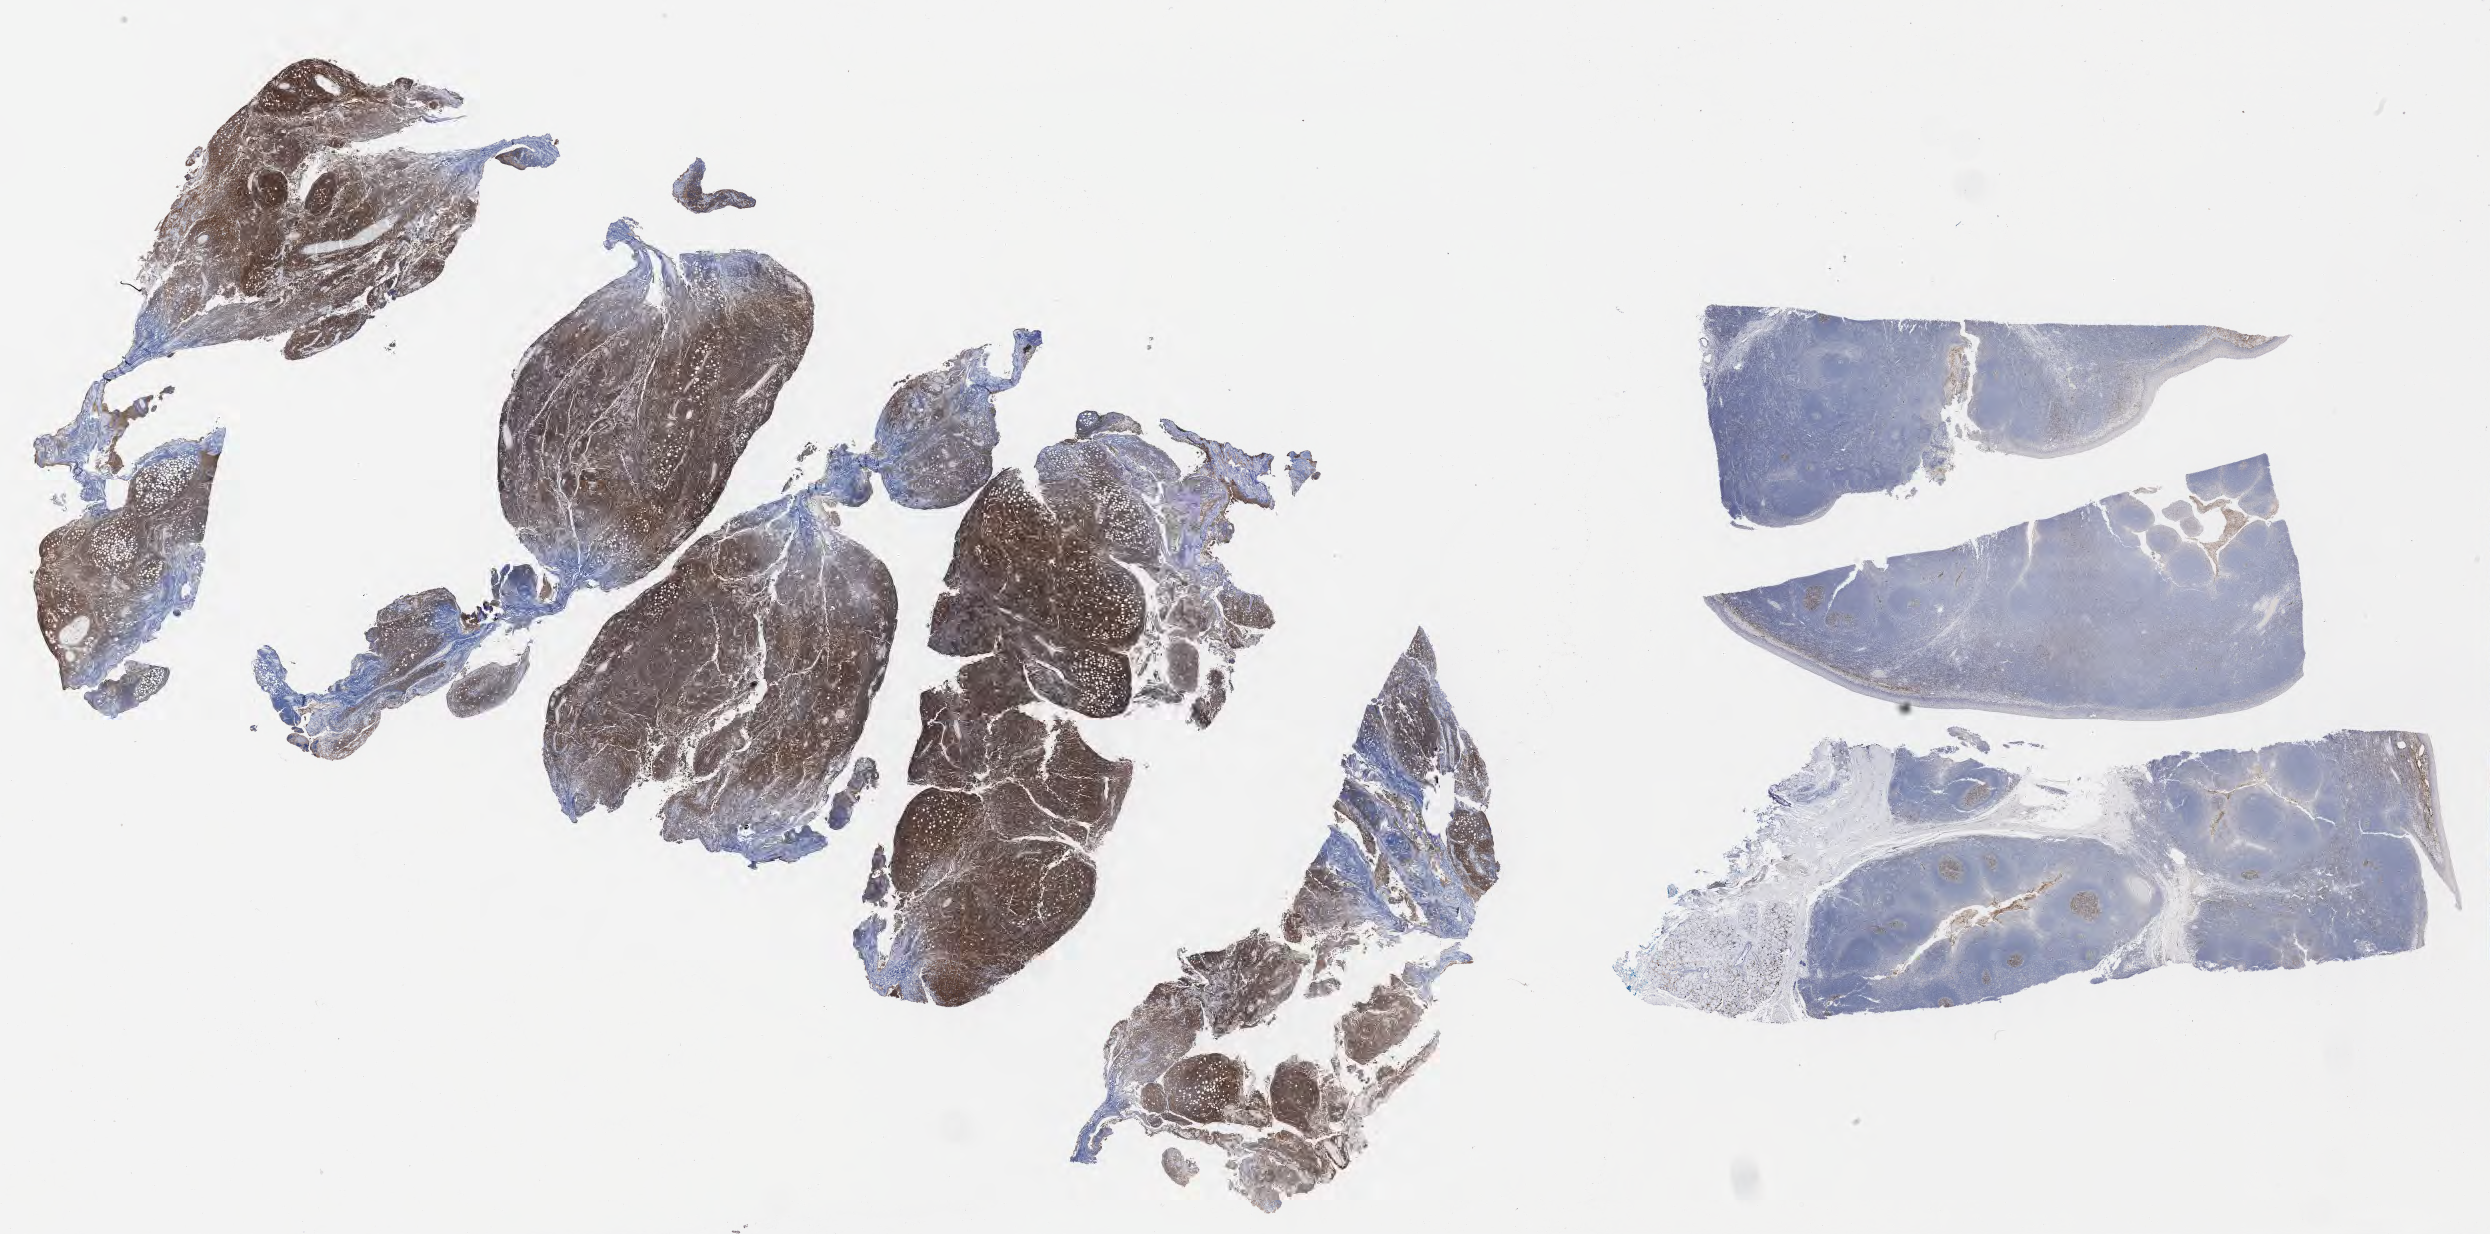
Whole-slide image, immunohistochemical stain for CD10, low-resolution overview of the scanned area, about 40.2 x 19.9 mm; specimen: tumor tissue; anatomic site: peritoneum. Patient: male, age at initial diagnosis 8 years.
Diagnosis: Burkitt lymphoma, NOS.